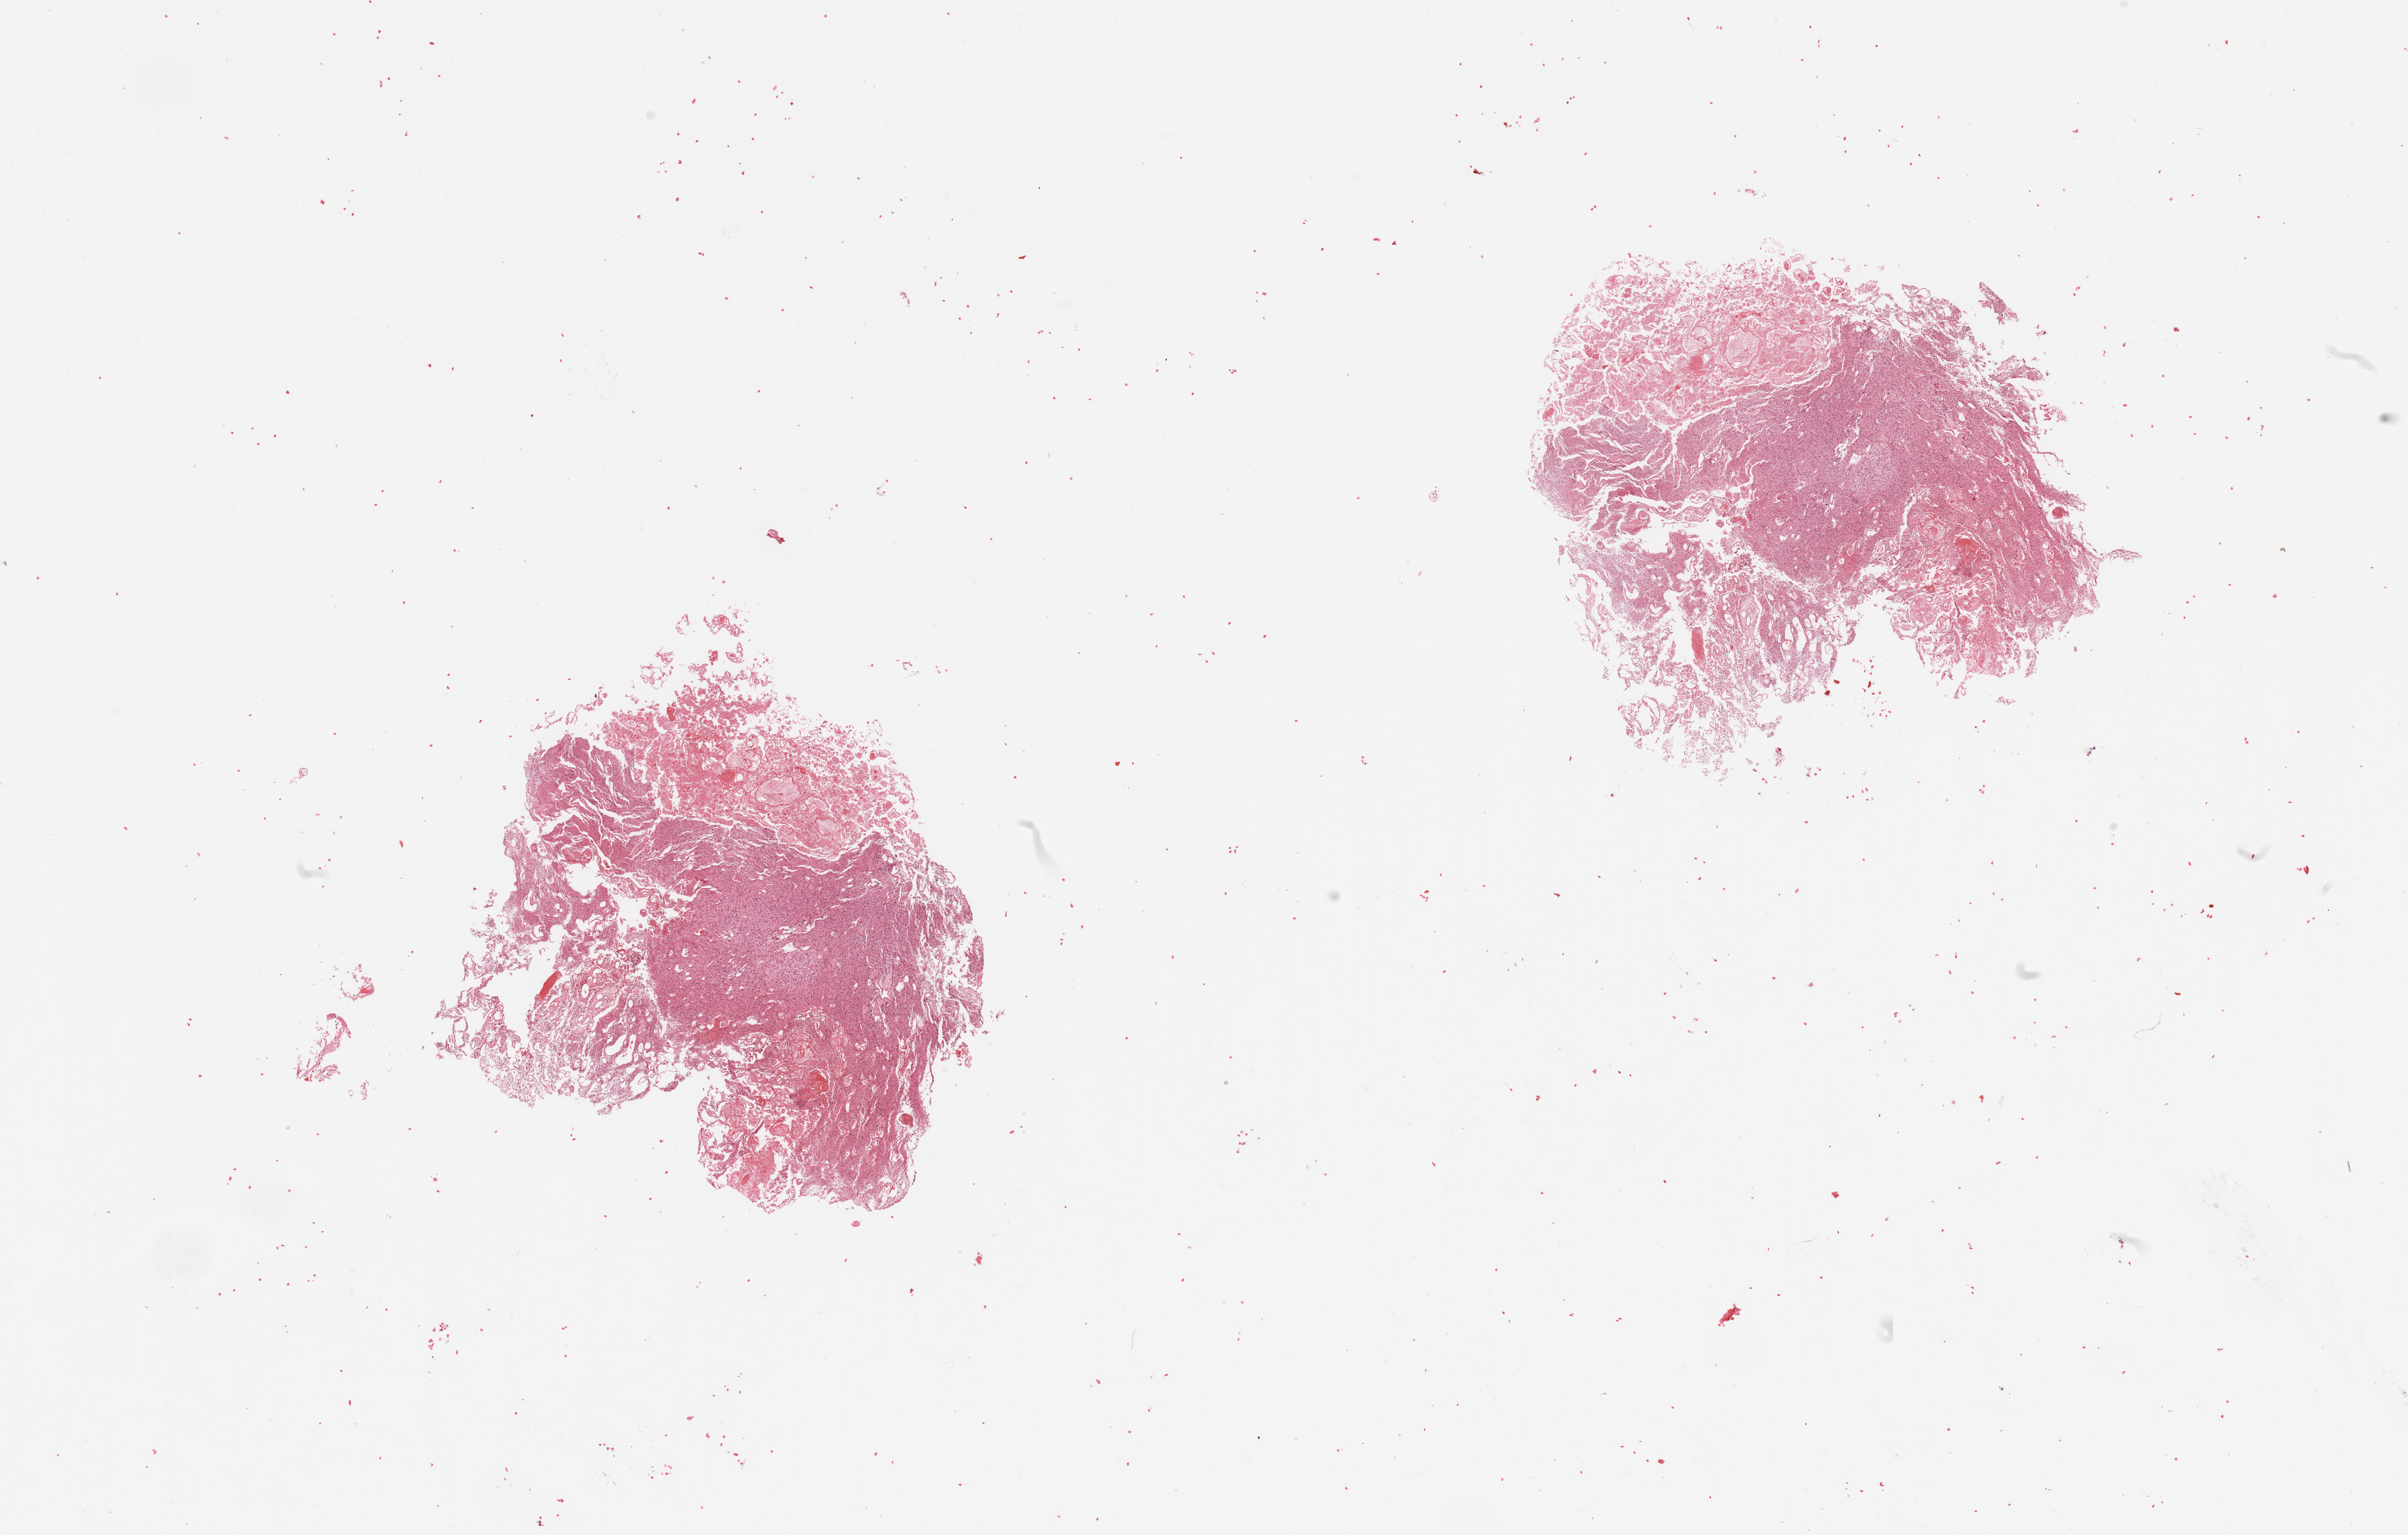
H&E whole-slide image, shown as a low-resolution overview of the whole scanned area (about 27.6 x 17.6 mm, from a 20x scan), brain, tumour tissue. Patient: male, age 39 years.
Primary tumour site (as recorded): frontal lobe. Histologic diagnosis: Glioblastoma.